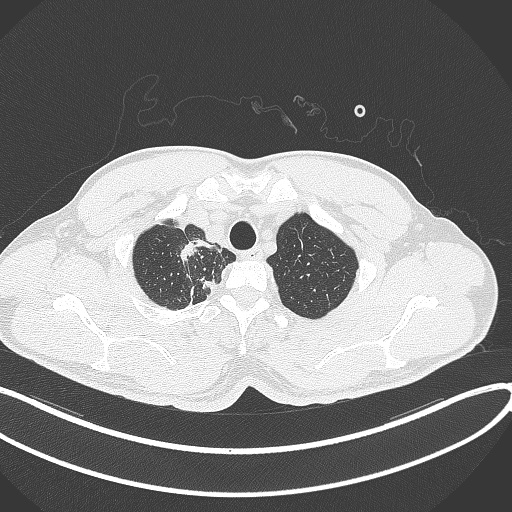
Chest CT, one axial slice; slice 335 of 391 in the series (ordered by position); reconstruction kernel B70f; 120 kVp; lung window (W 1500 / L -600 HU); 1 mm slice thickness; 512 × 512 image matrix, field of view 400 × 400 mm. Patient: male, 48 years. Case-level facts recorded for this patient, not image findings: clinical TNM (as recorded): T1c N1 M1.
Annotated regions visible in this slice (rectangle marked by the reading radiologist):
- lung tumour (recorded histology: adenocarcinoma): bounding box <177,239,199,264> (left, top, right, bottom; pixels)